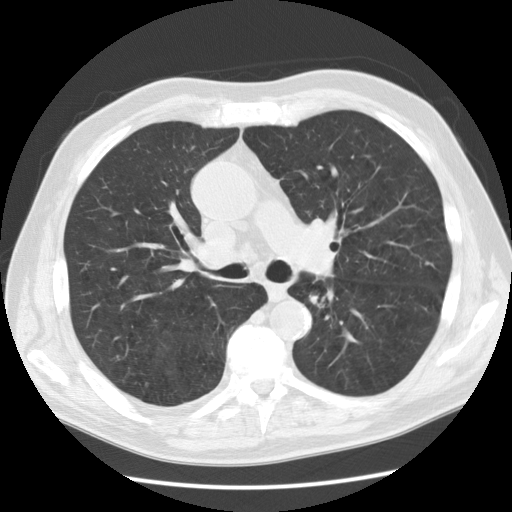
Low-dose screening chest CT, one axial slice; slice 80 of 130 in the series (ordered by position); reconstruction kernel STANDARD; 120 kVp; lung window (W 1500 / L -600 HU); 512 × 512 image matrix.
Structures marked on this image (expert manual segmentation):
- lesion 1 (tumor, lower lobe of left lung): bounding box (x1, y1, x2, y2) in pixels: (311, 290, 328, 306)